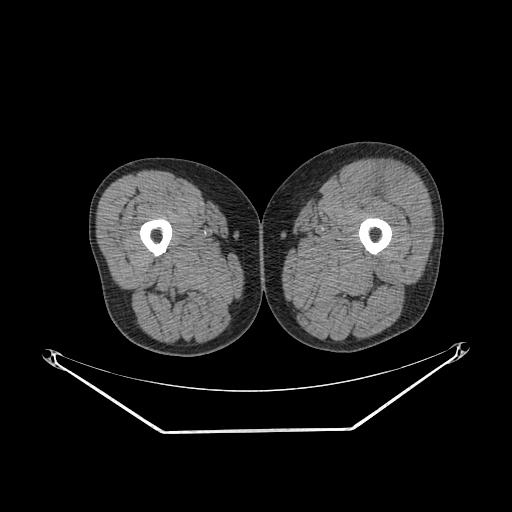
CT of an extremity soft-tissue mass (from a PET/CT study), one axial slice; slice 222 of 267 in the series (ordered by position); 140 kVp; soft-tissue window (W 400 / L 40 HU); 512 × 512 image matrix, field of view 500 × 500 mm. Male patient. Case-level facts recorded for this patient, not image findings: histological type: extraskeletal osteosarcoma; grade: high; site of the primary tumour: thigh.
Outlined on this slice (expert contour drawn on MRI and transferred to this co-registered scan by the dataset authors):
- gross tumour volume (mass): bounding box [x1, y1, x2, y2] px = [374, 174, 410, 204]